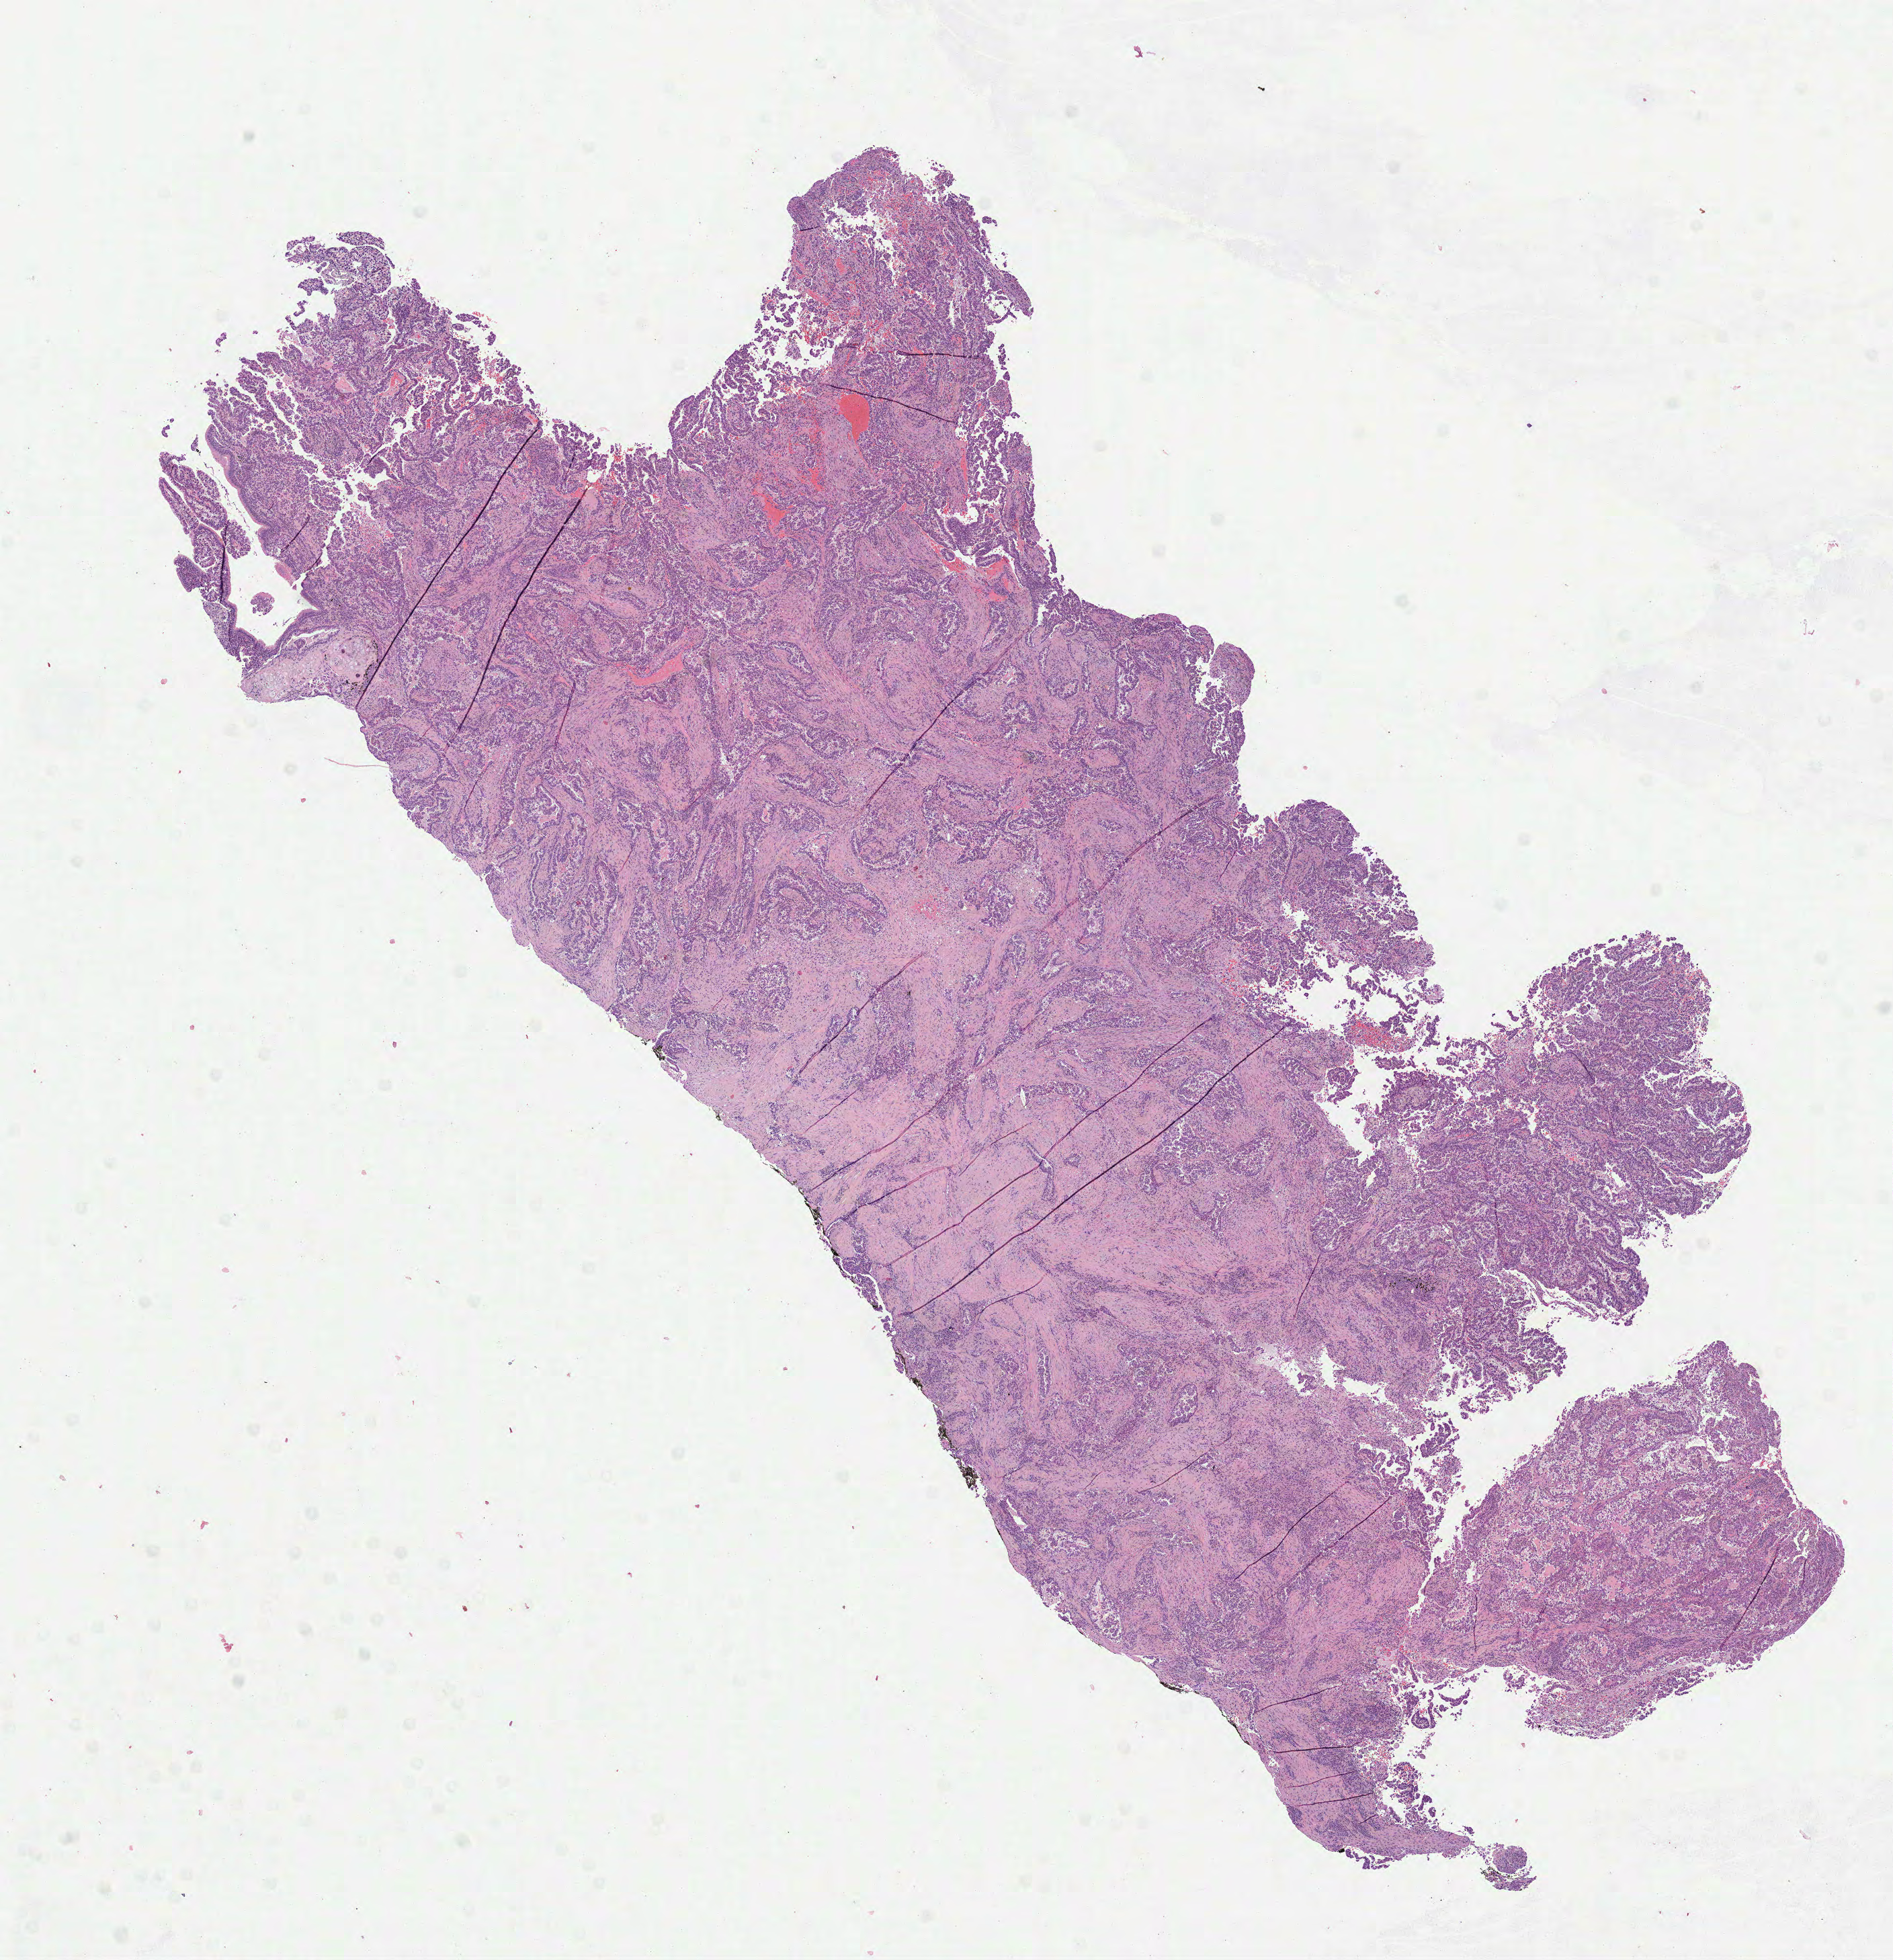
Whole-slide histology image, H&E — shown as a low-resolution overview of the whole scanned area (about 11.4 x 11.8 mm, from a 40x scan). Formalin-fixed paraffin-embedded (FFPE) diagnostic section. Lung, primary tumour sample. Patient: male, age at initial diagnosis 63 years.
Laterality: right. Histologic diagnosis: Adenocarcinoma, NOS (lower lobe, lung). AJCC pathologic stage: IB.